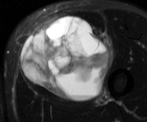
MRI of an extremity soft-tissue mass, one axial slice; position 31 of 52 along the scan axis; T2-weighted fat-saturated; MR volume resampled by the dataset authors to the PET/CT grid (not the native acquisition matrix); 147 × 122 image matrix, field of view 144 × 119 mm. Male patient. Case-level facts recorded for this patient, not image findings: histological type: pleiomorphic liposarcoma; grade: high; site of the primary tumour: left thigh.
Annotated regions visible in this slice (expert contour drawn on MRI and transferred to this co-registered scan by the dataset authors):
- gross tumour volume including surrounding oedema: bounding box <21,14,113,99> (left, top, right, bottom; pixels)
- gross tumour volume (mass): <21,14,110,100>